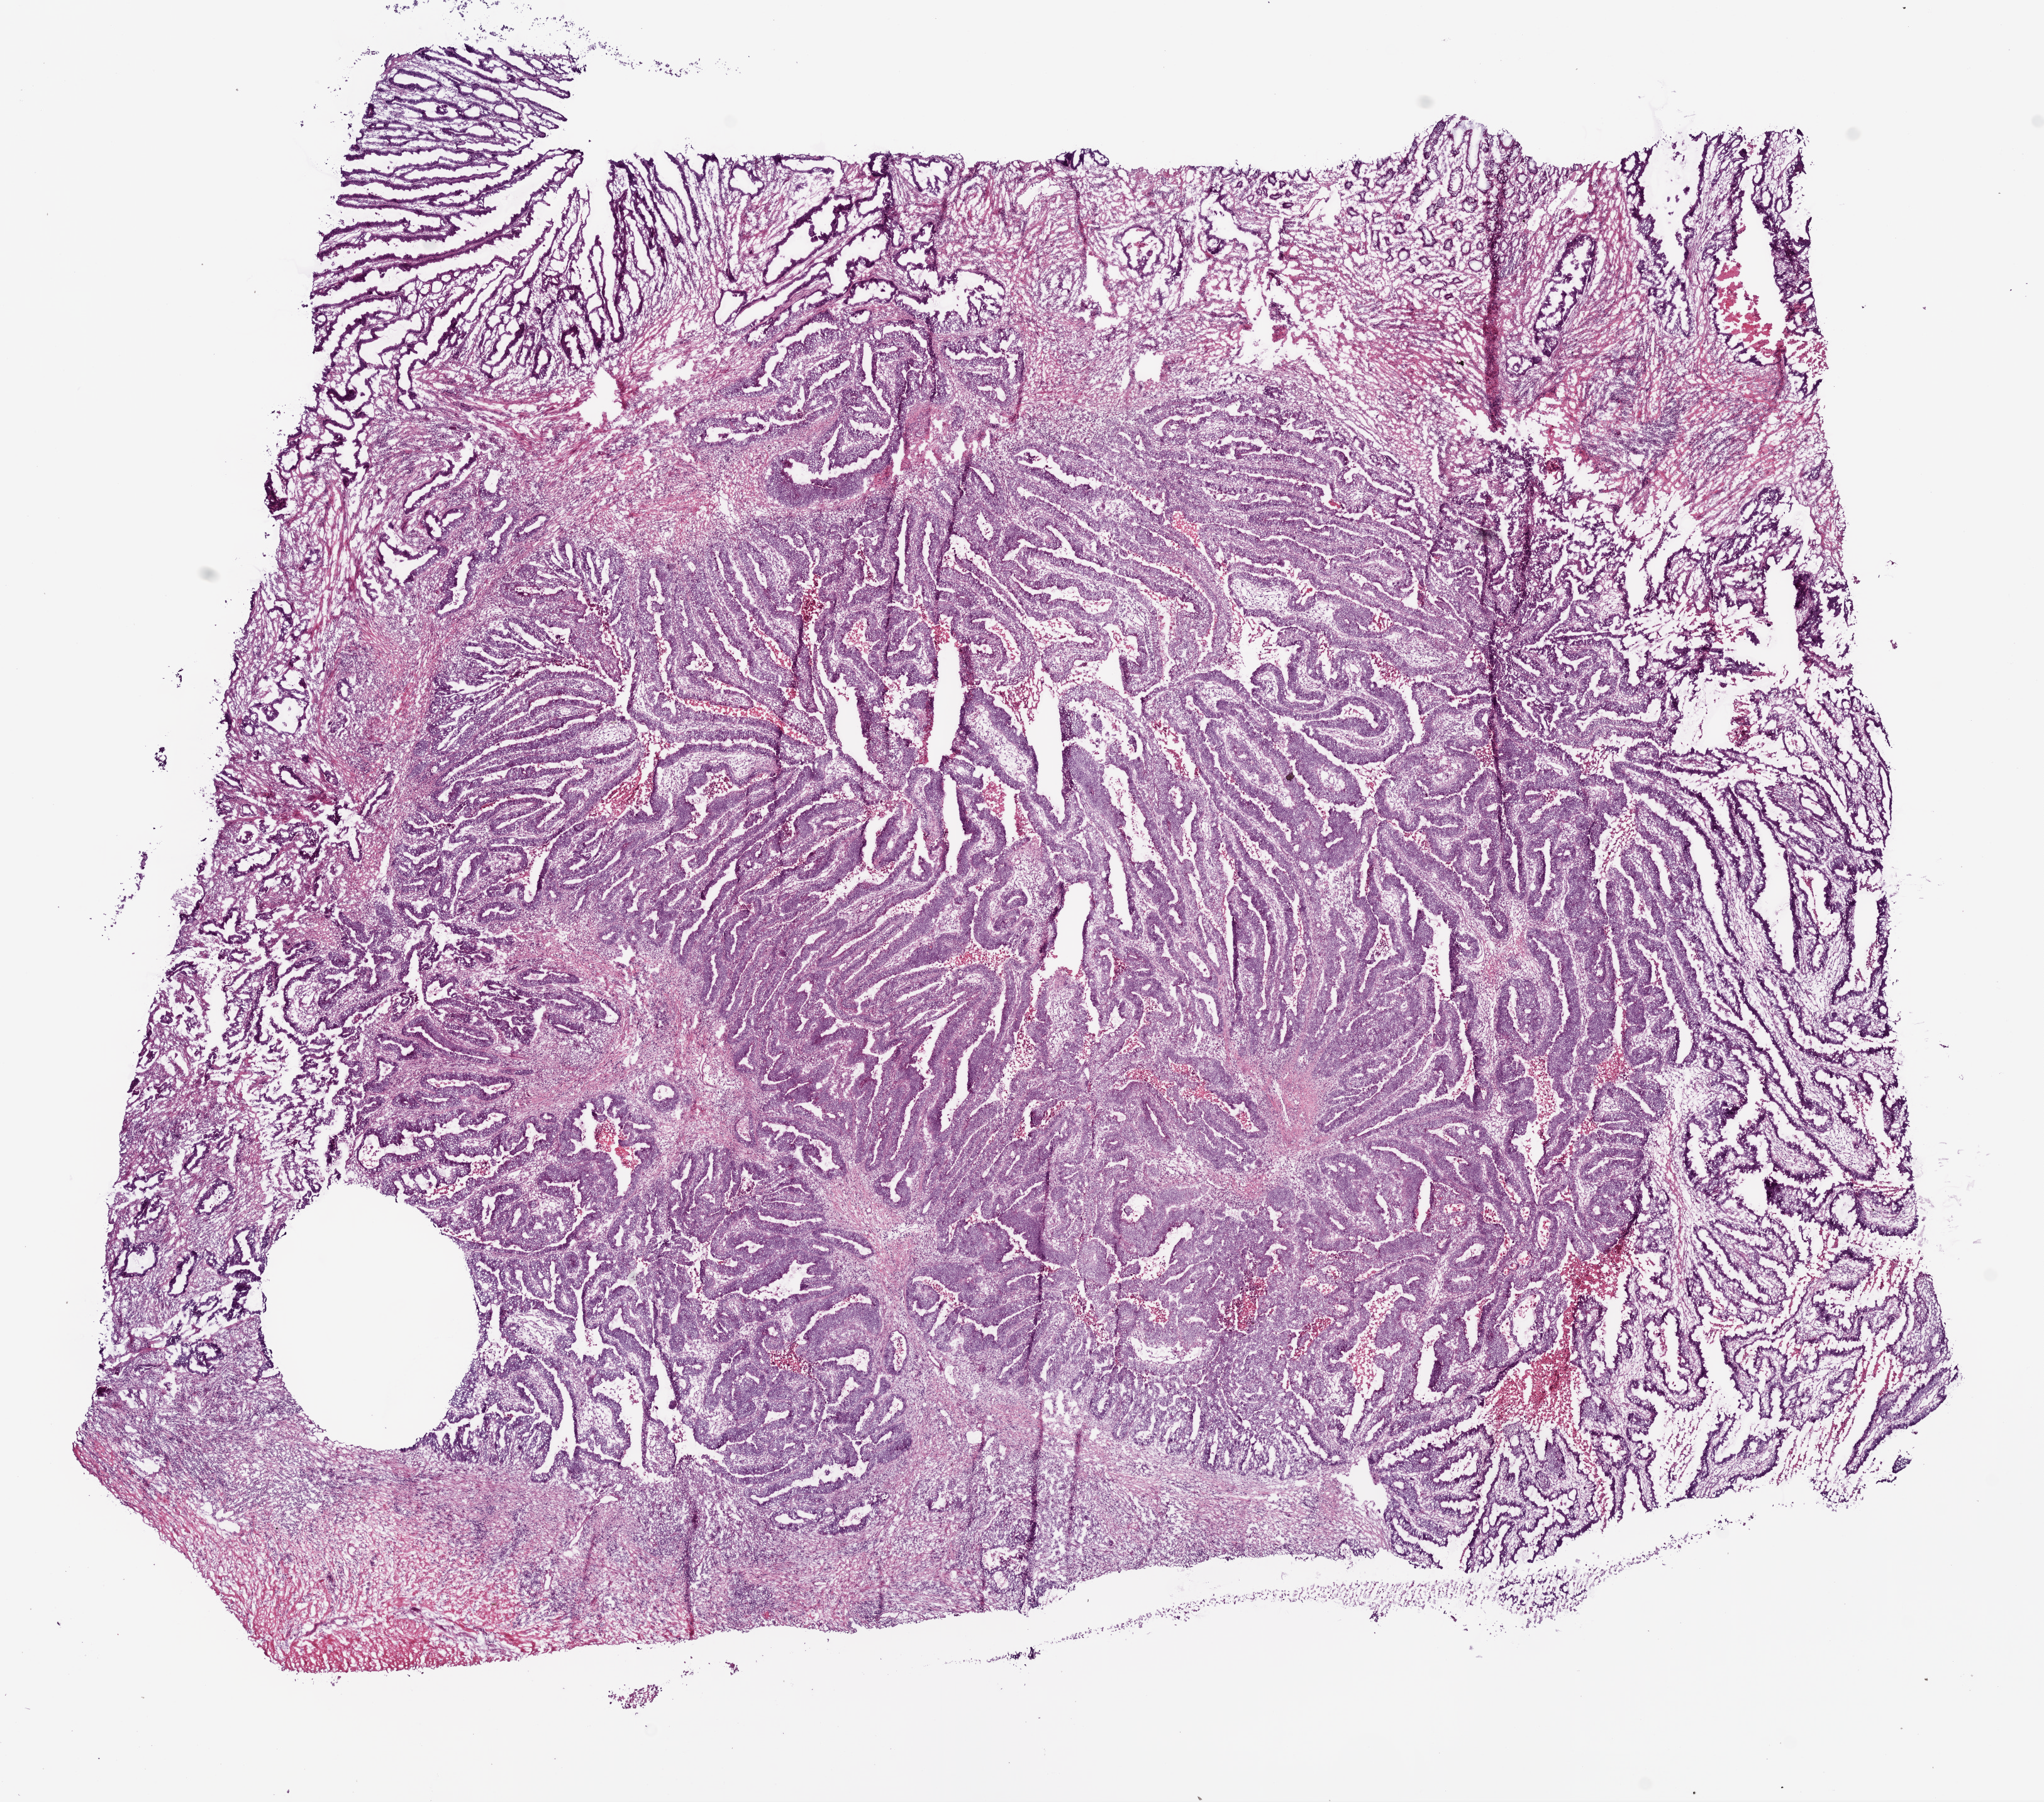
Digitized H&E tissue section (whole slide), shown as a low-resolution overview of the whole scanned area (about 13.0 x 11.5 mm, from a 20x scan), frozen section, sample: primary tumour, colon. Female patient; age at initial diagnosis 54 years. Composition of this section per pathologist review: tumour cells 75%, tumour nuclei 80%, normal cells 5%, stromal cells 15%, necrosis 5%.
Pathologic diagnosis: Adenocarcinoma, NOS. AJCC pathologic stage: IIA.